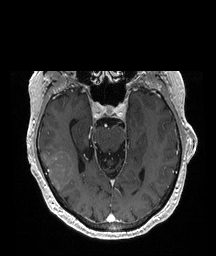
Brain MRI from a brain-tumour surgery series, one axial slice; slice 131 of 208 in the series (ordered by position); T1-weighted post-contrast; 216 × 256 image matrix, field of view 216 × 256 mm. Case-level facts recorded for this patient, not image findings: histopathology: Glioblastoma; WHO grade: 4; IDH mutation: no.
Structures marked on this image (expert manual segmentation):
- tumour: bounding box (x1, y1, x2, y2) in pixels: (44, 151, 75, 192)